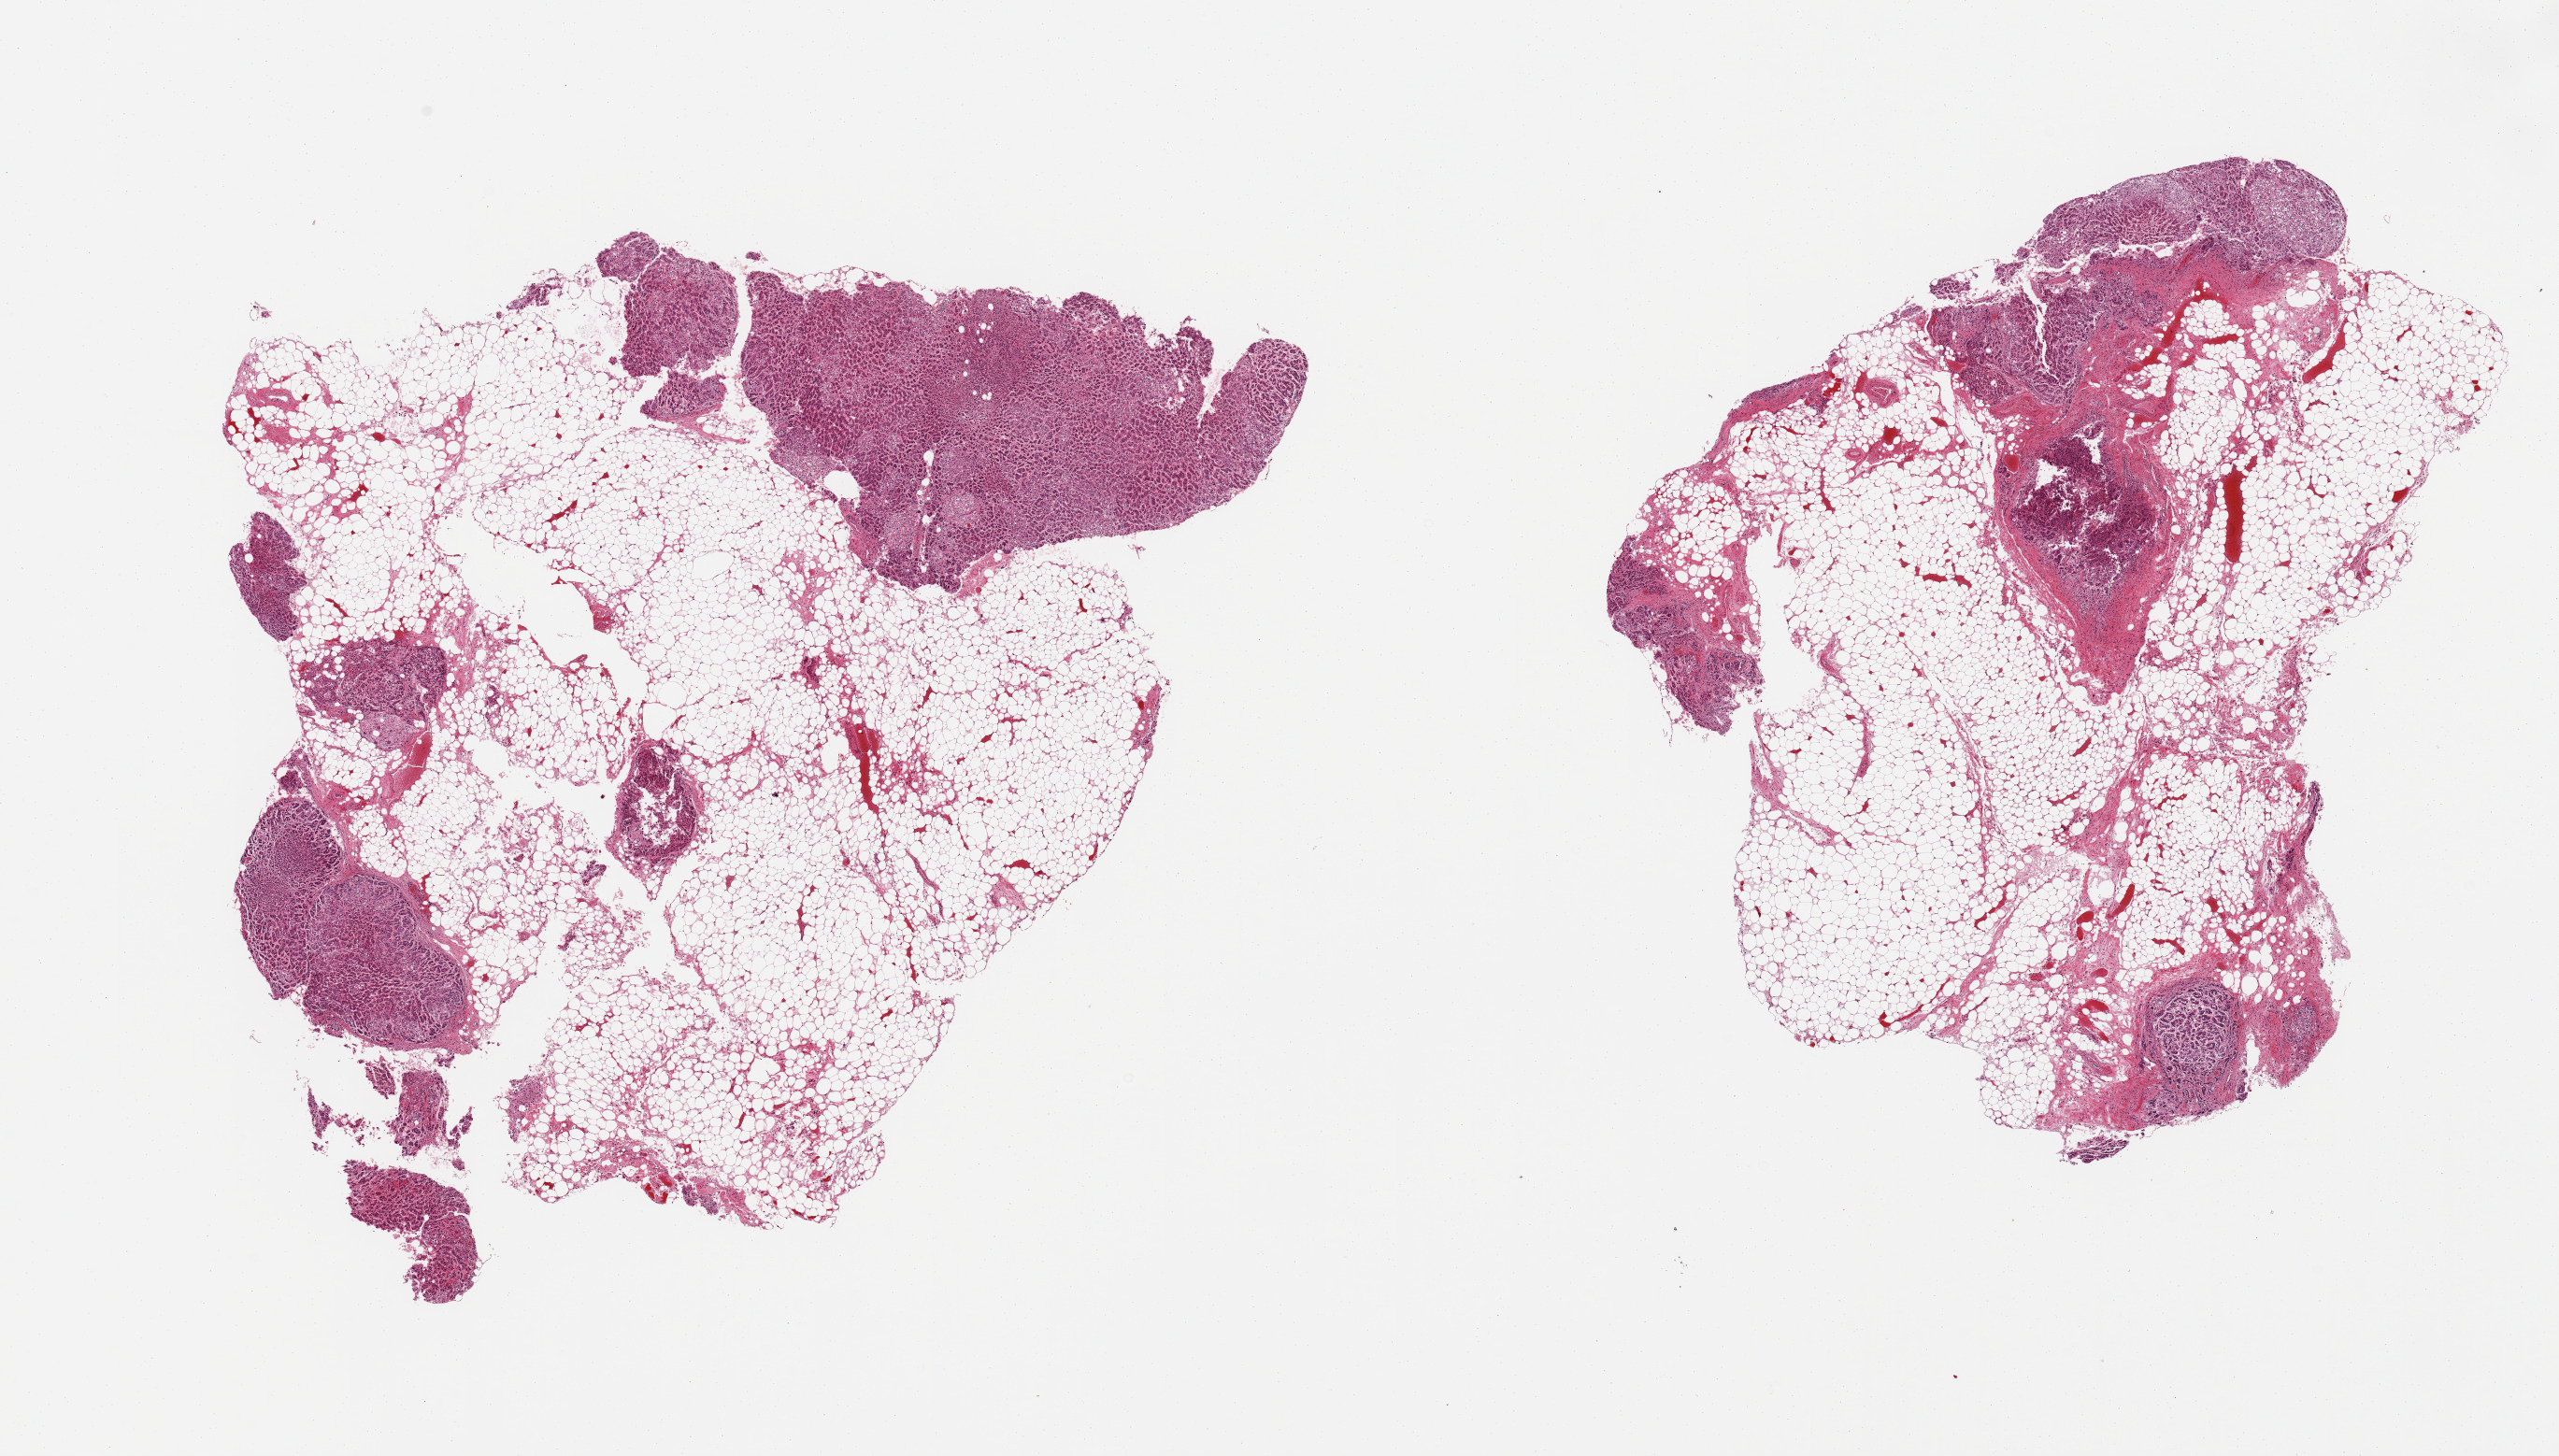
Hematoxylin and eosin (H&E) whole-slide image — shown as a low-resolution overview of the whole scanned area (about 21.7 x 12.3 mm), PAXgene-fixed, paraffin-embedded tissue, target tissue: adrenal gland, donor tissue sample.
- pathologist's review note for this sample: 2 pieces; 80% fat